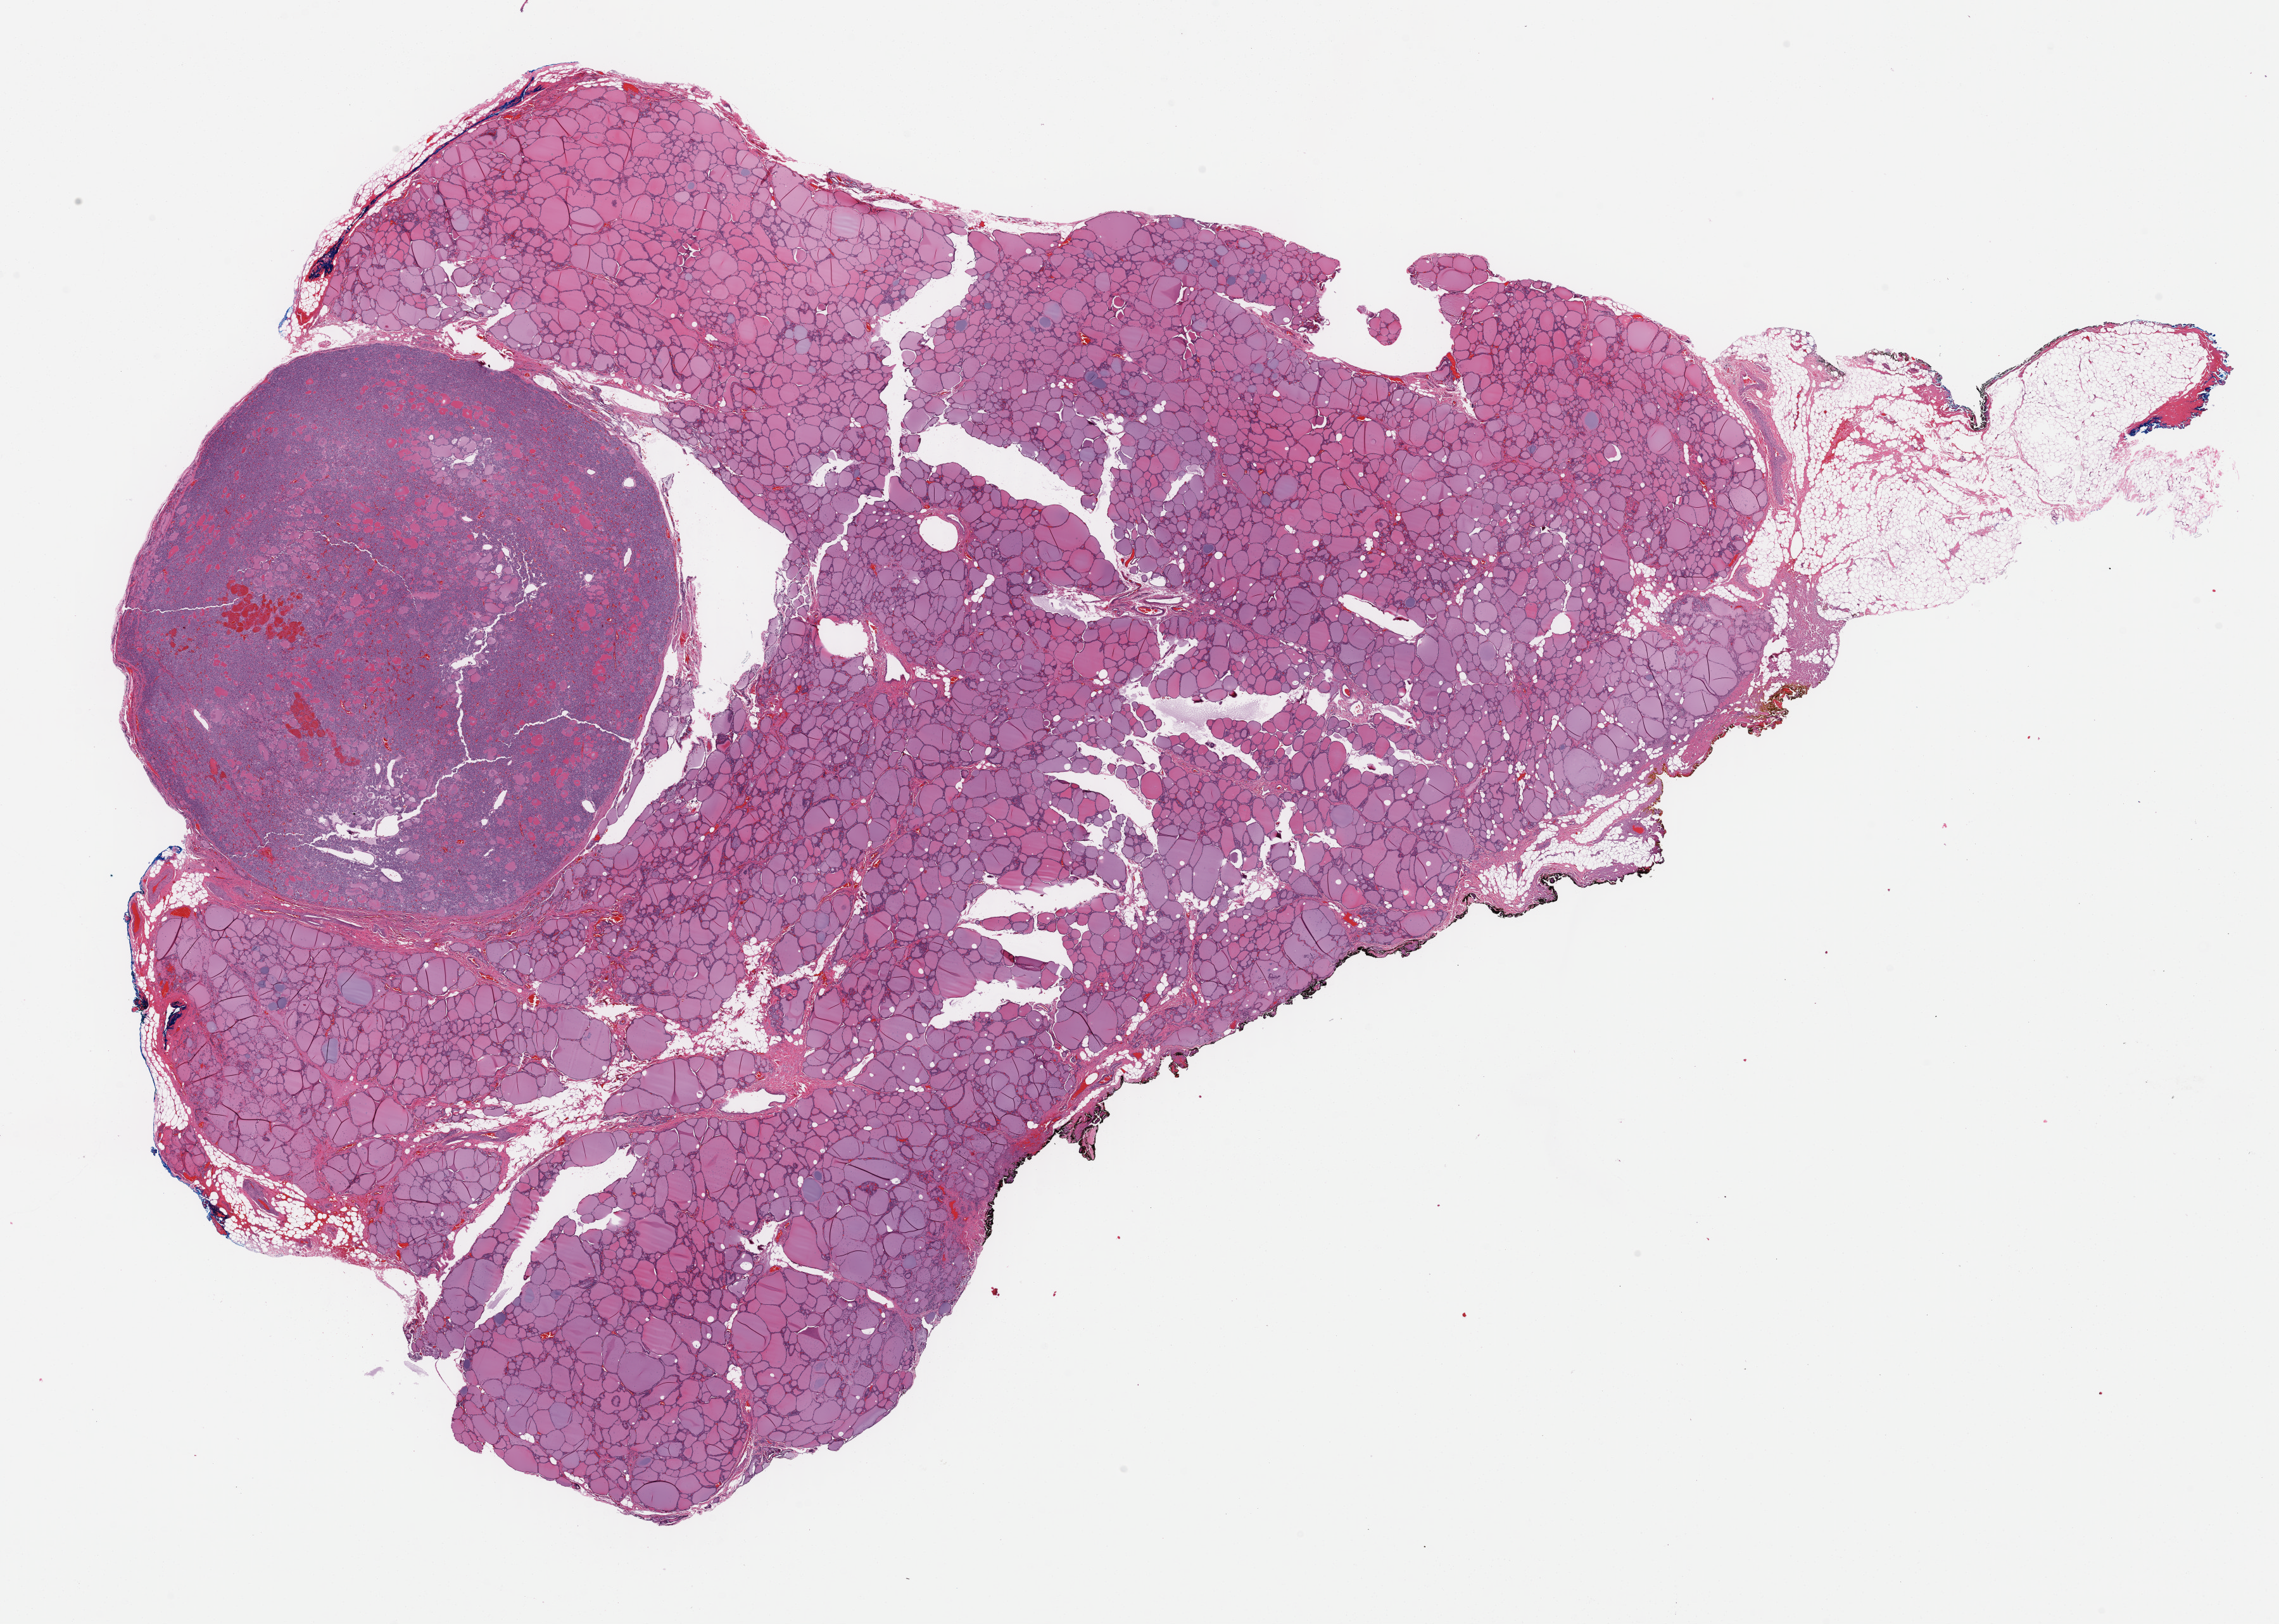
Digitized H&E-stained tissue section (whole slide), low-resolution overview of the scanned area, about 28.4 x 20.2 mm (acquisition: 40x scan). Formalin-fixed paraffin-embedded (FFPE) diagnostic section. Sample: primary tumour, thyroid. Male patient; age at initial diagnosis 40 years.
* AJCC pathologic stage: I (7th edition)
* histologic diagnosis: Papillary carcinoma, follicular variant
* laterality: left
* TNM: T1b N0 M0
* lymph nodes positive (case pathology): 0 of 1 examined